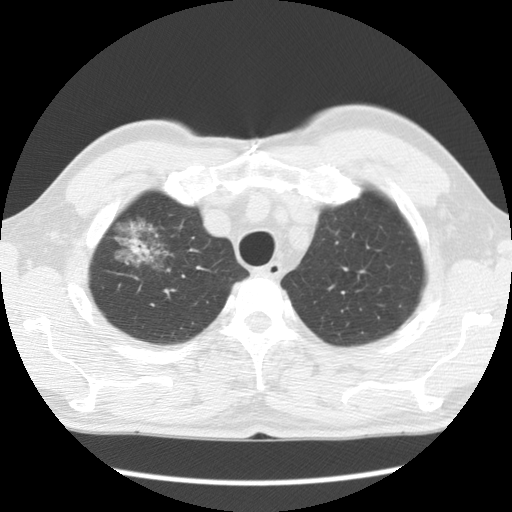
Chest CT (low-dose screening protocol), one axial image. Baseline annual screen. Lung window (W 1500 / L -600 HU). 2.5 mm slice thickness. 120 kVp. 512 × 512 image matrix. Male, age 64 years at enrolment. Former smoker at enrolment.
Lesion marked by an expert reader, bounding box [x1, y1, x2, y2] px = [102, 206, 175, 278]. The screening reader recorded 2 non-calcified nodules or masses ≥4 mm on this exam (right upper lobe, left upper lobe); which of them this box marks is not recorded. Official screen result: positive, change unspecified: nodule(s) >= 4 mm or enlarging nodule(s), mass(es), or other non-specific abnormalities suspicious for lung cancer. Later outcome: lung cancer diagnosed 750 days after this screen — adenocarcinoma, NOS, right upper lobe, well differentiated (G1), stage IB (AJCC 6th edition), 45 mm at pathology.